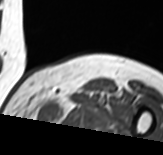
MRI of an extremity soft-tissue mass, one axial slice; MR volume resampled by the dataset authors to the PET/CT grid (not the native acquisition matrix); 3.27 mm slice thickness; 163 × 155 image matrix, field of view 159 × 151 mm. Female patient. Case-level facts recorded for this patient, not image findings: histological type: pleomorphic leiomyosarcoma; grade: high; site of the primary tumour: left thigh.
Structures marked on this image (expert contour drawn on MRI and transferred to this co-registered scan by the dataset authors):
- gross tumour volume including surrounding oedema: box from (x=39, y=99) to (x=74, y=123) px